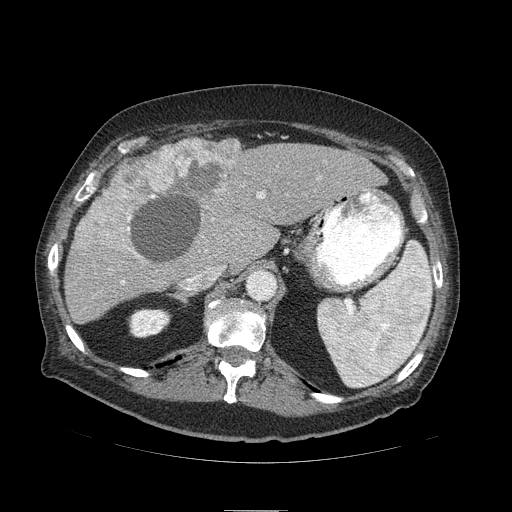
Contrast-enhanced abdominal CT (liver protocol), one axial slice; slice 63 of 103 in the series (ordered by position); 120 kVp; soft-tissue window (W 400 / L 40 HU); 512 × 512 image matrix, field of view 440 × 440 mm. Case-level facts recorded for this patient, not image findings: diagnosis: hepatocellular carcinoma (patient treated with transarterial chemoembolisation; whether this scan precedes or follows treatment is not stated here); TNM stage (as recorded): Stage-IIIA; Child-Pugh class: B; tumour differentiation: well differentiated; tumour nodularity: multinodular.
Outlined on this slice (semi-automatic segmentation, software-assisted and operator-edited):
- liver parenchyma outside the tumour (the mass and vessels are separate outlines, so this box may not span the whole liver): bounding box <64,140,386,324> (left, top, right, bottom; pixels)
- mass: <78,137,242,250>
- liver vessels: <122,192,264,283>